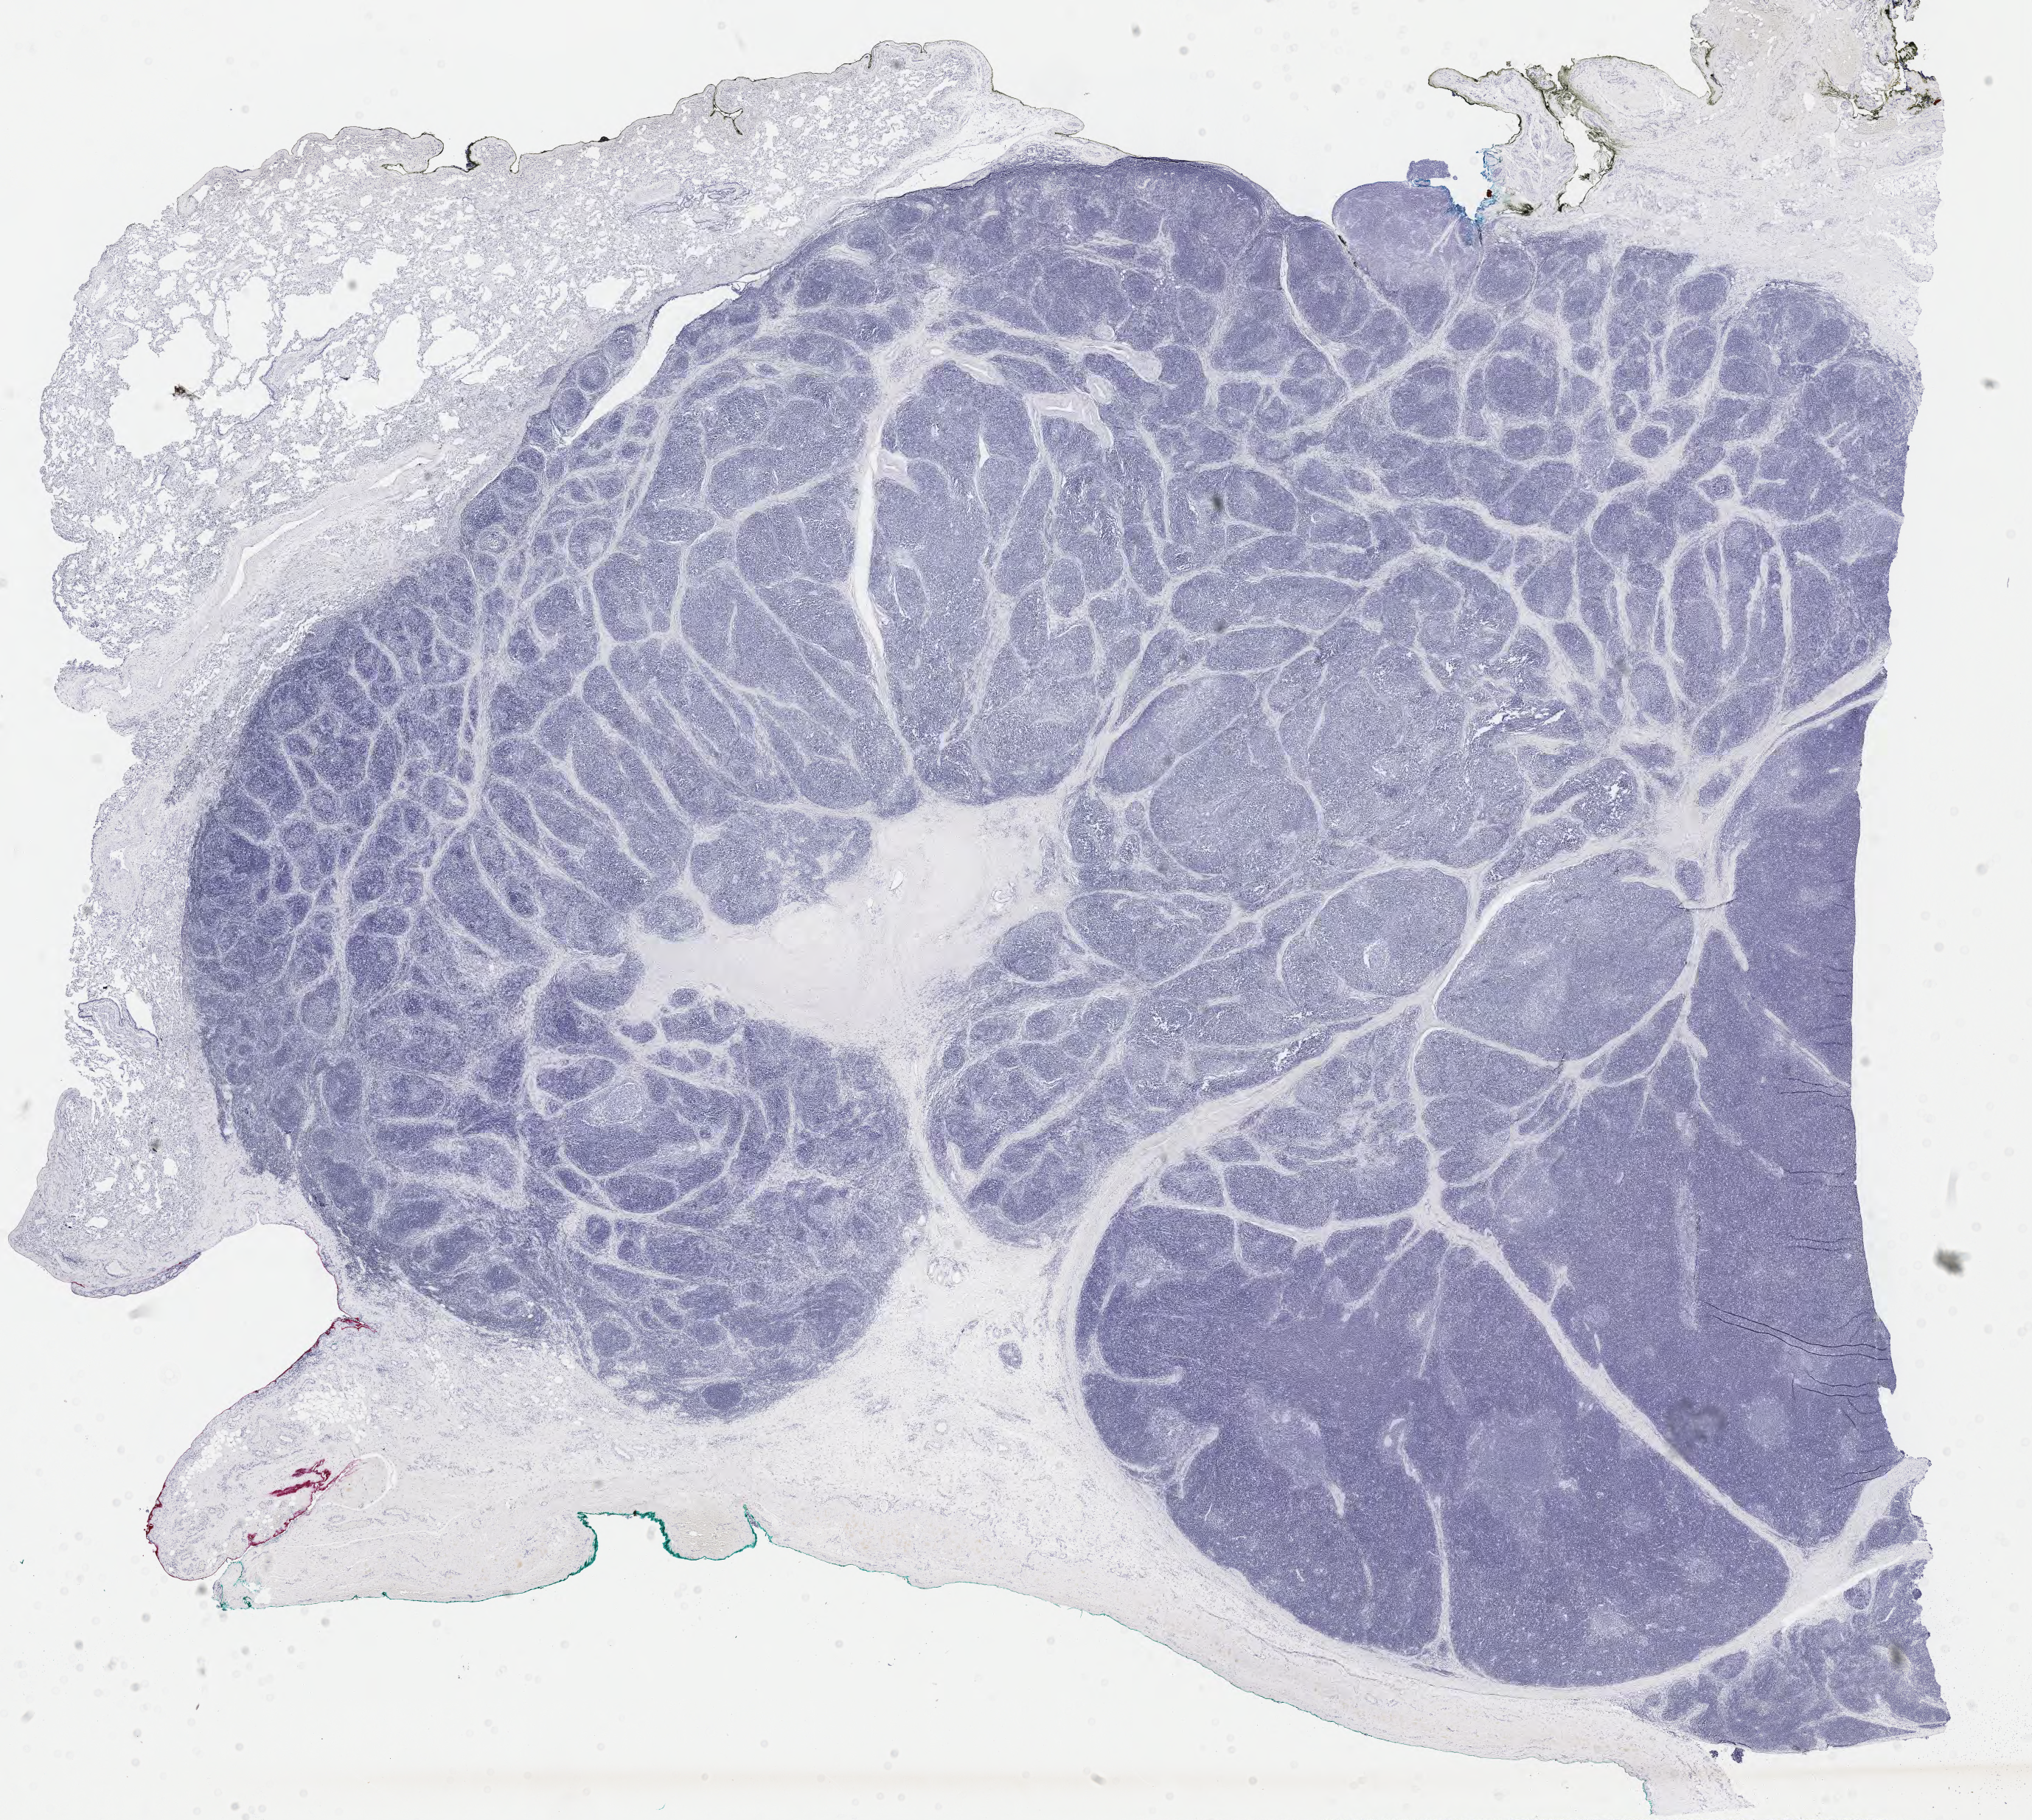
Digitized H&E tissue section (whole slide), low-resolution overview of the scanned area, about 21.8 x 19.6 mm (acquisition: 40x scan). Formalin-fixed paraffin-embedded (FFPE) diagnostic section. Thymus, primary tumour sample. Female, age 57 years at initial diagnosis.
Histologic diagnosis: Thymoma, type B1, NOS.